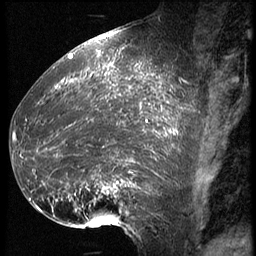
Breast MRI (dynamic contrast-enhanced), one sagittal slice; position 26 of 62 along the scan axis; 3 images stored at this slice position (order not interpretable as contrast timing); 1.5 T; TE 4.2 ms, TR 9 ms; 2.5 mm slice thickness; 256 × 256 image matrix, field of view 180 × 180 mm. Patient: female, 39 years. Case-level facts recorded for this patient, not image findings: setting: breast cancer imaged before/during neoadjuvant chemotherapy; receptor status: HER2-positive.
Outlined on this slice (semi-automatically segmented with operator editing):
- analysis volume of interest (the breast-tissue region the enhancement analysis was run in; not a lesion): bounding box <16,64,171,228> (left, top, right, bottom; pixels)
- tumour enhancement mask (voxels above the 140 % enhancement threshold inside the analysis volume of interest): <16,64,171,217>